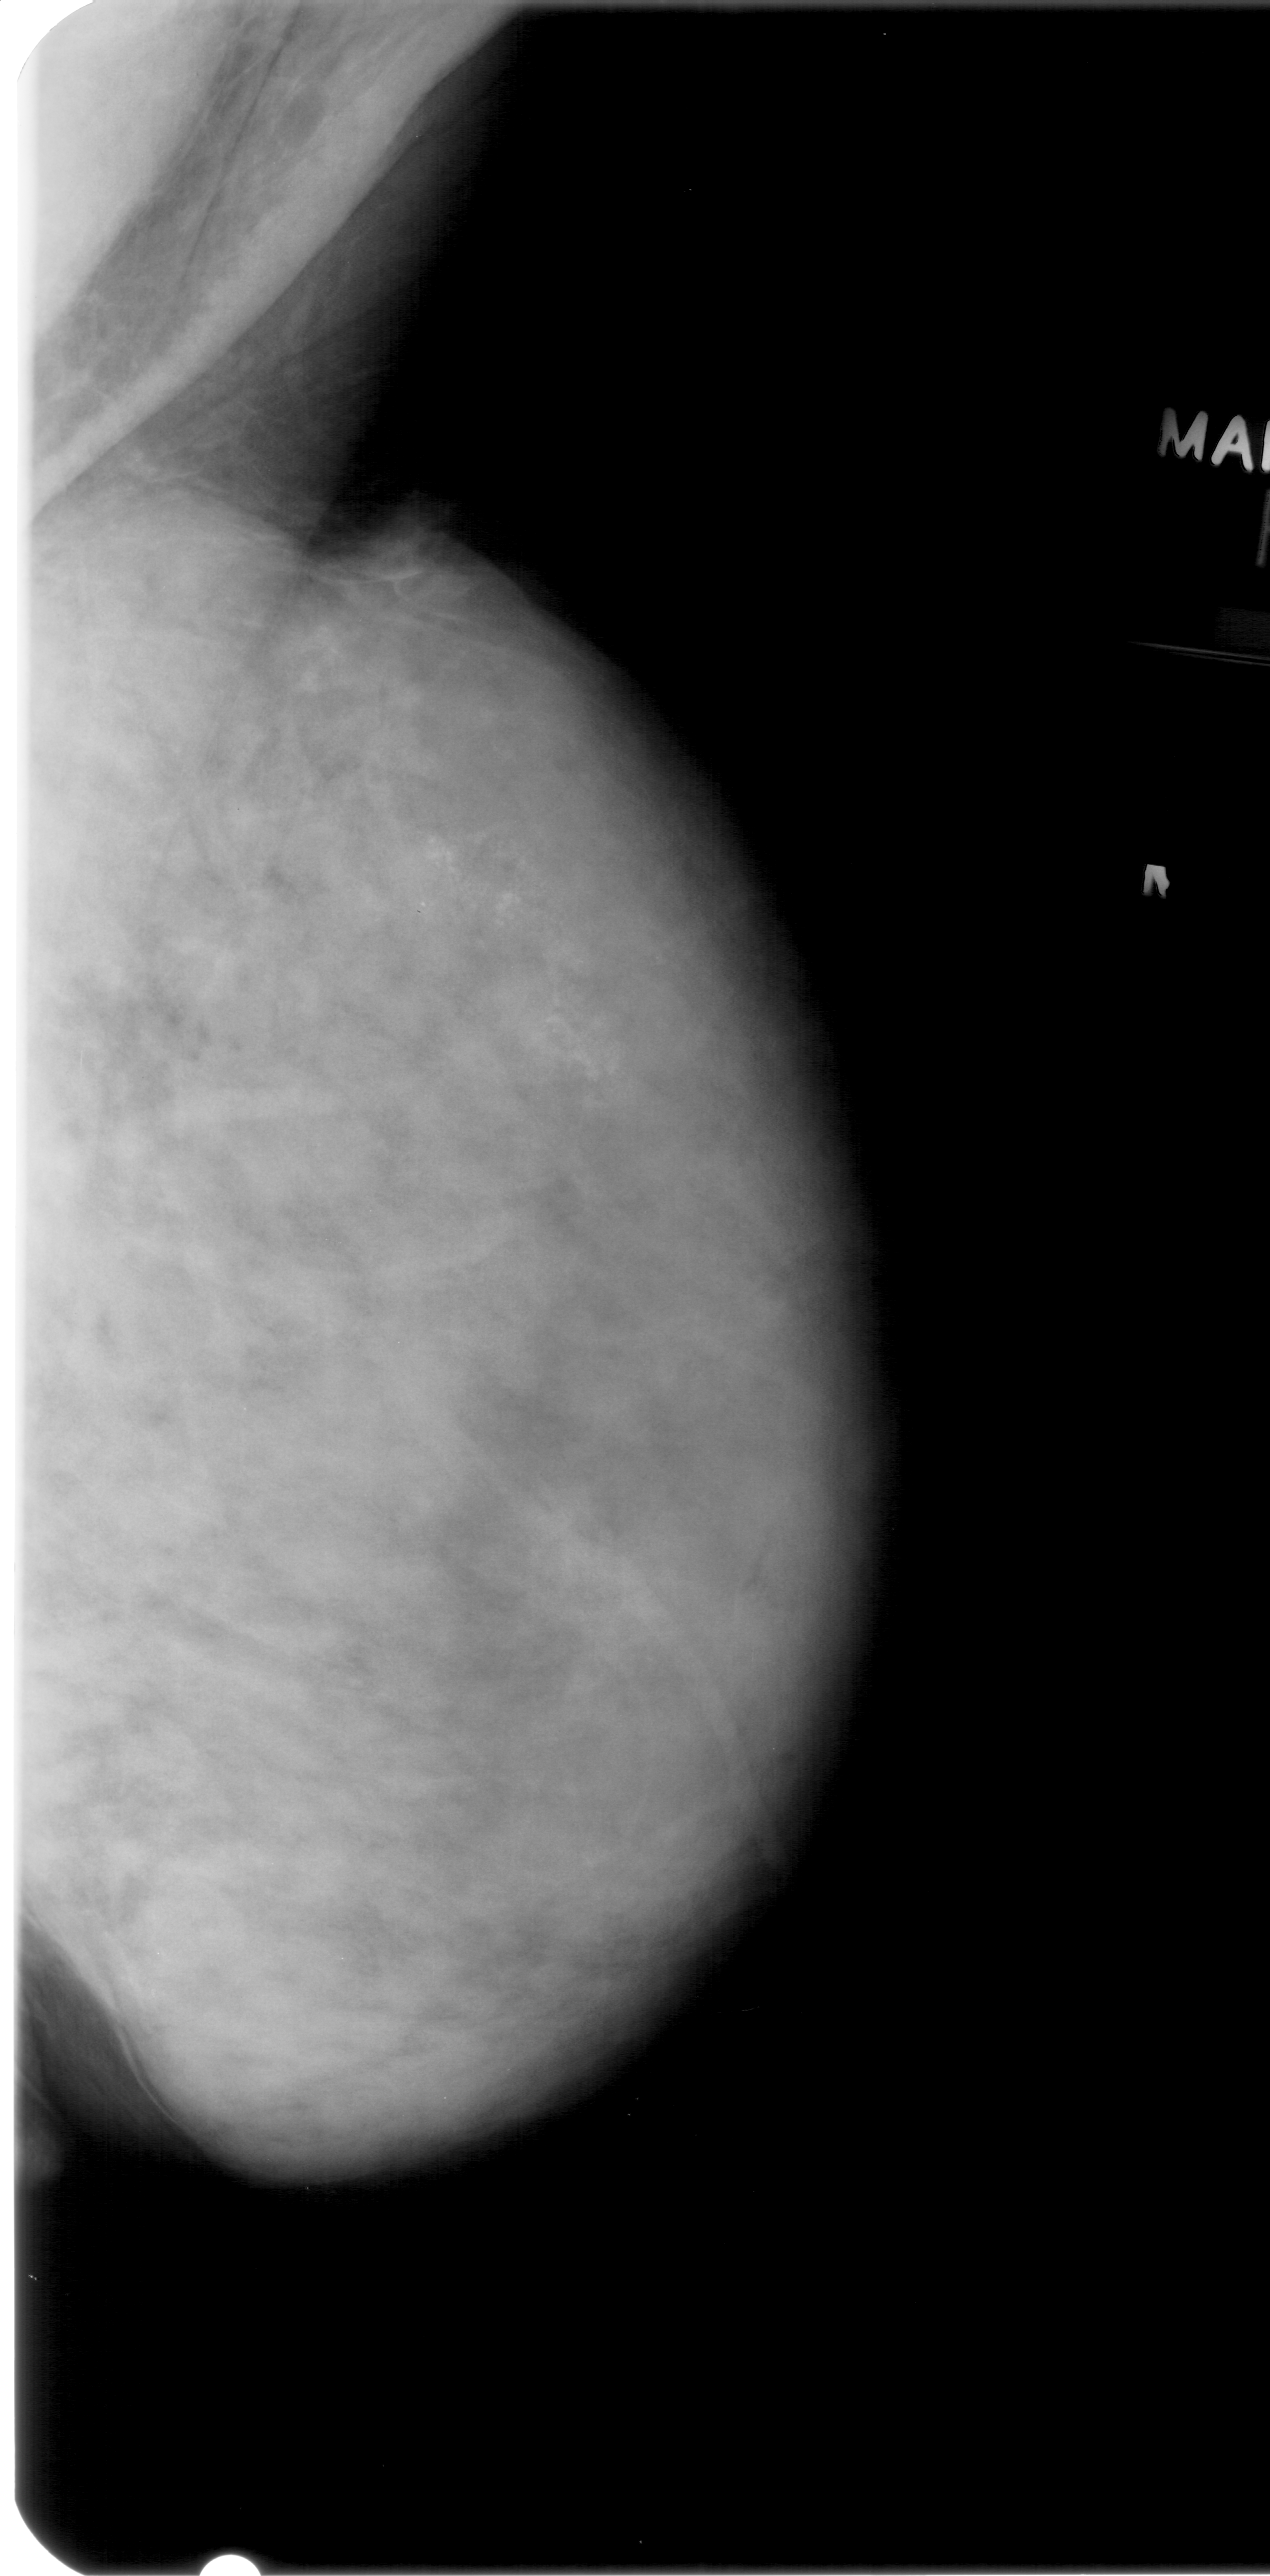
Digitized screen-film mammogram; right breast; mediolateral oblique (MLO) view.
Calcifications, morphology amorphous, distribution segmental; BI-RADS assessment category 4; pathology (as recorded): benign.